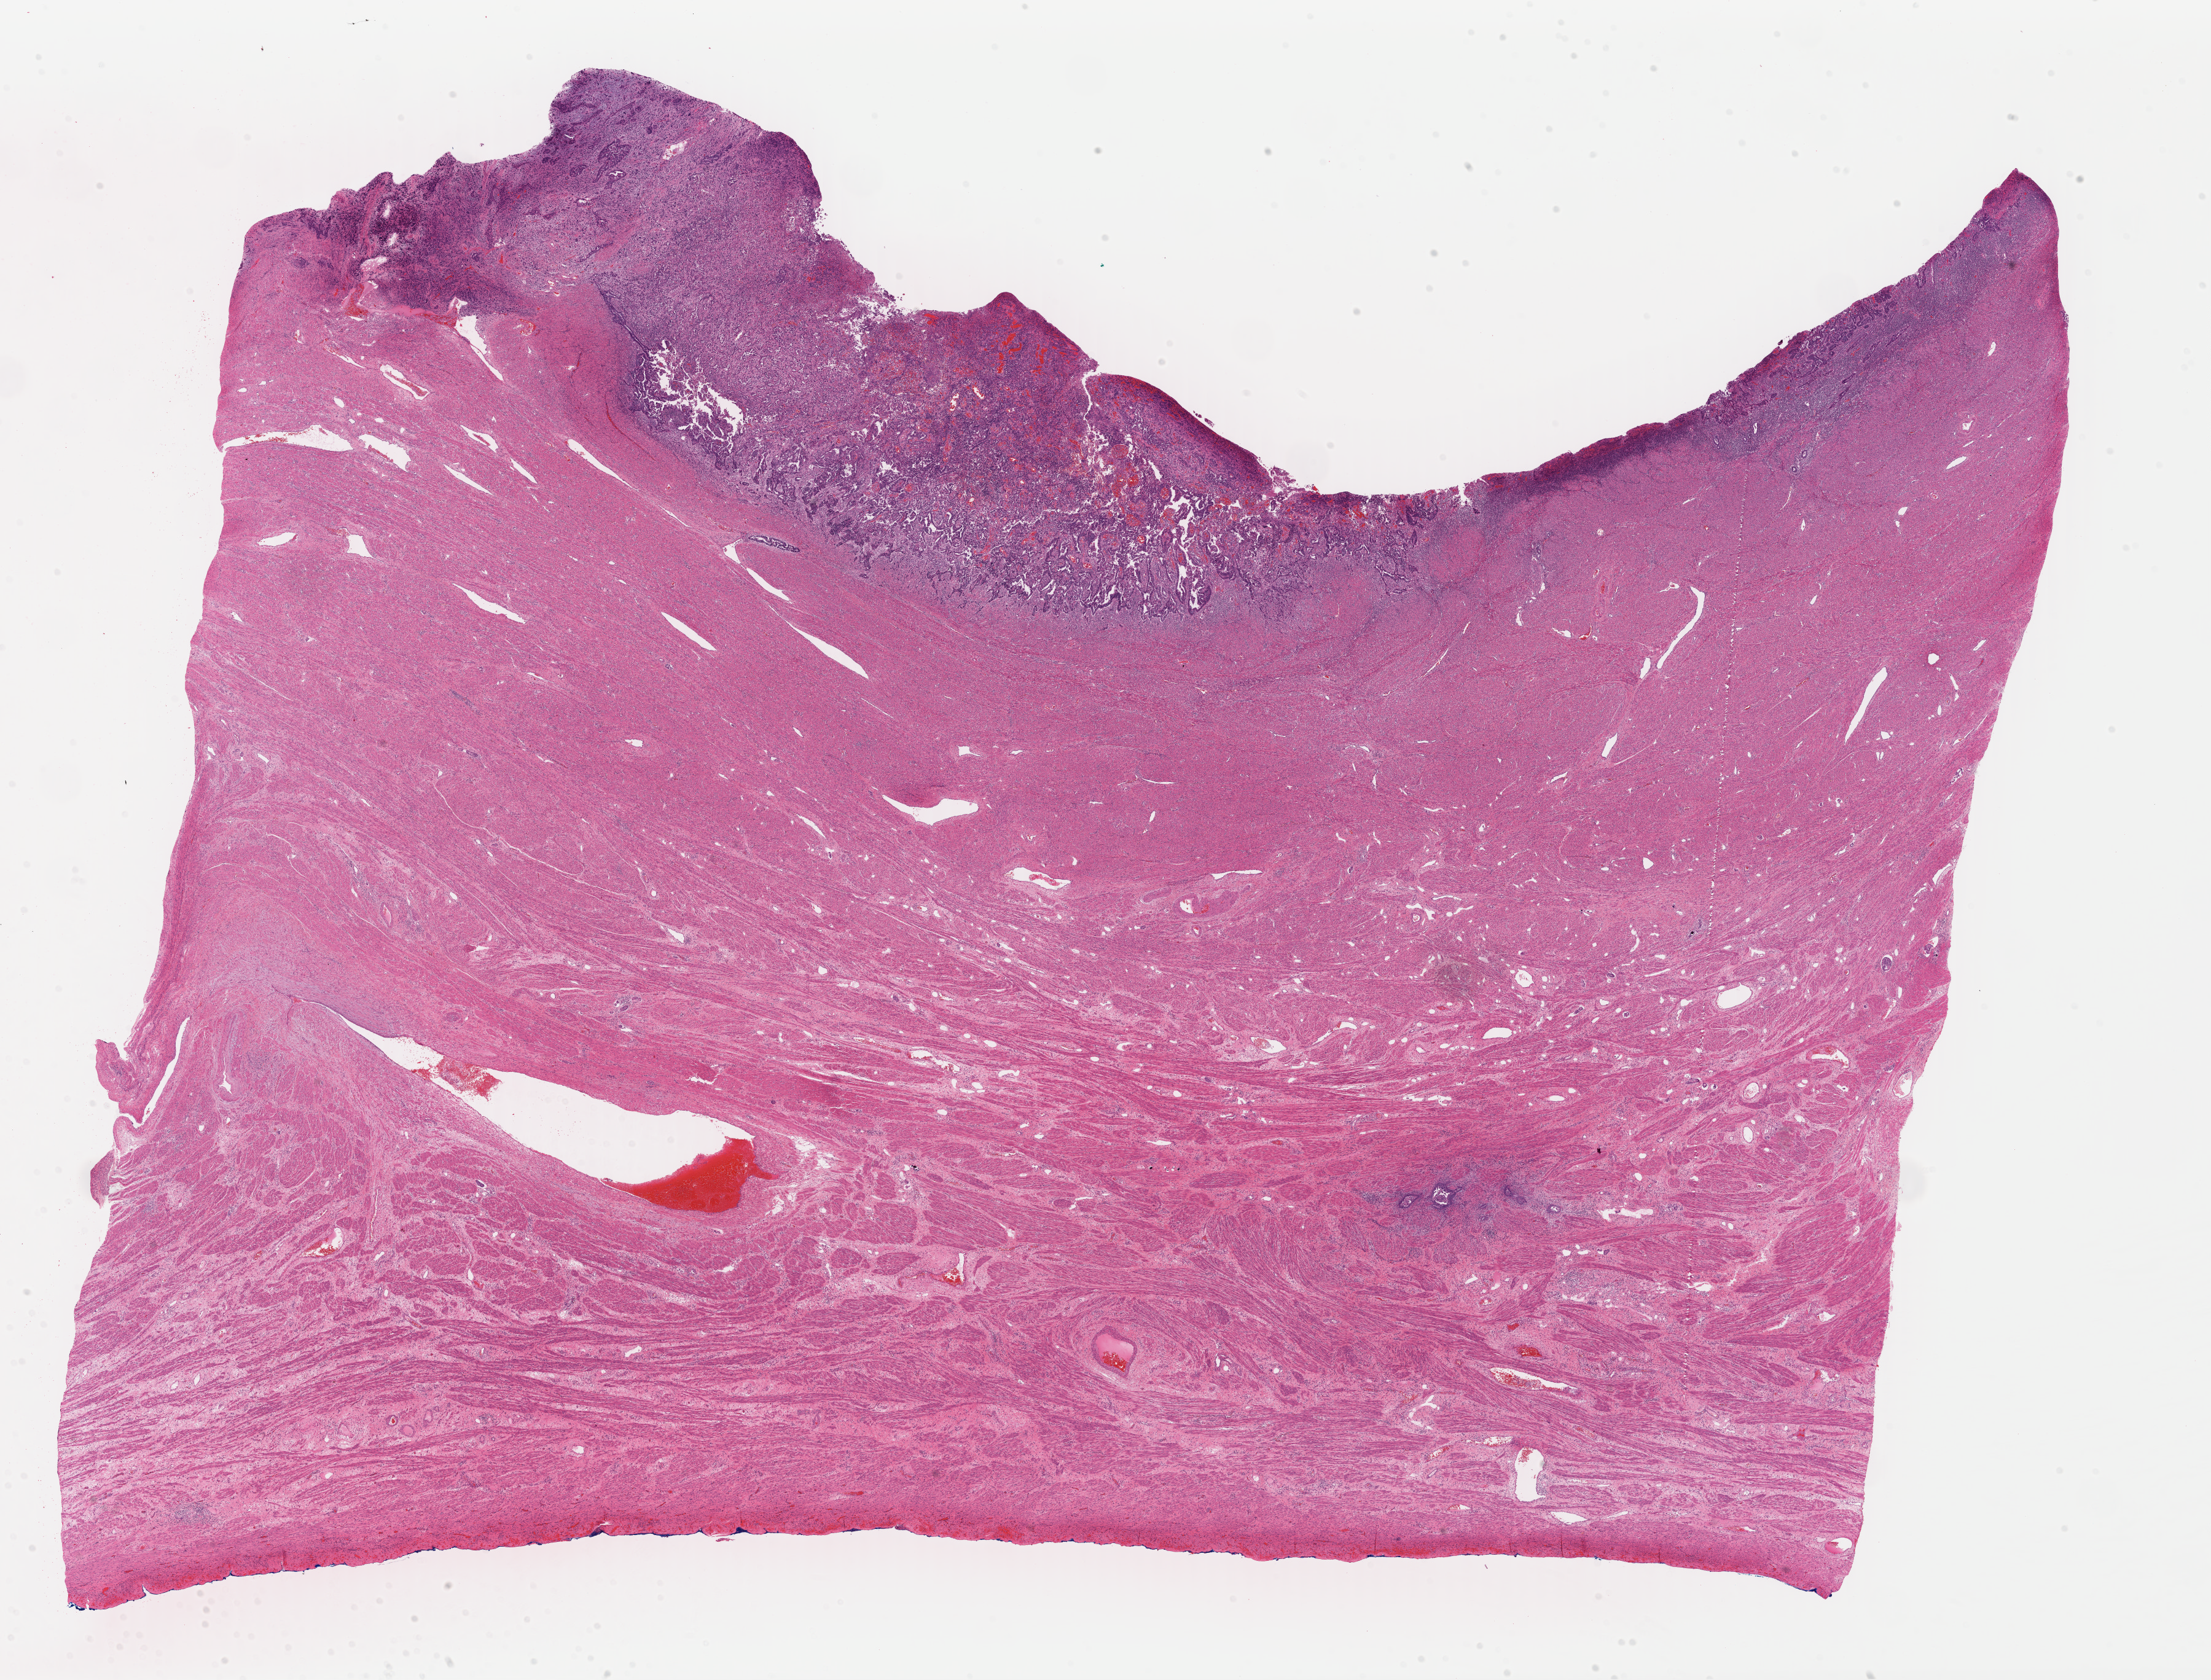
Digitized Hematoxylin and eosin (H&E) stained tissue section (whole slide), shown as a low-resolution overview of the whole scanned area (about 28.3 x 21.5 mm); formalin-fixed paraffin-embedded (FFPE) diagnostic section; uterus, primary tumour sample. Patient: female, age at initial diagnosis 67 years.
Histologic diagnosis: Mullerian mixed tumor (endometrium). FIGO stage: IIIC.